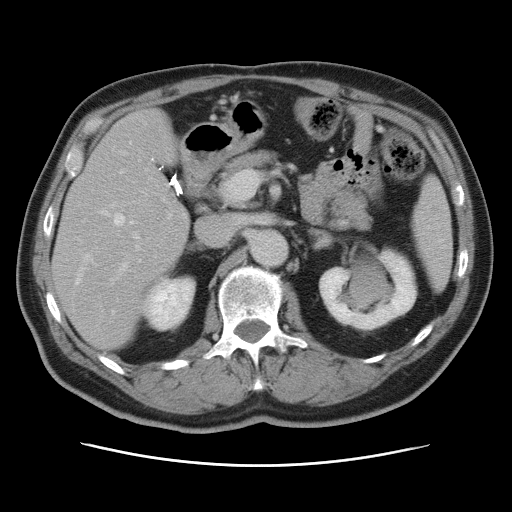
Contrast-enhanced abdominal CT, one axial slice; position 41 of 80 along the scan axis; 120 kVp; soft-tissue window (W 400 / L 40 HU); 5 mm slice thickness; 512 × 512 image matrix. Male patient, age 69 years. Case-level facts recorded for this patient, not image findings: diagnosis: colorectal cancer liver metastases, imaged before liver resection; multiple liver metastases: no; largest metastasis: 5 cm; chemotherapy before resection: no.
Structures marked on this image (outlined manually by an expert reader):
- hepatic veins: box from (x=75, y=210) to (x=140, y=315) px
- liver: (x=55, y=110)–(x=188, y=349)
- planned liver remnant (the part of the liver to remain after resection): (x=54, y=188)–(x=188, y=349)
- portal vein (with intrahepatic branches): (x=111, y=171)–(x=171, y=282)